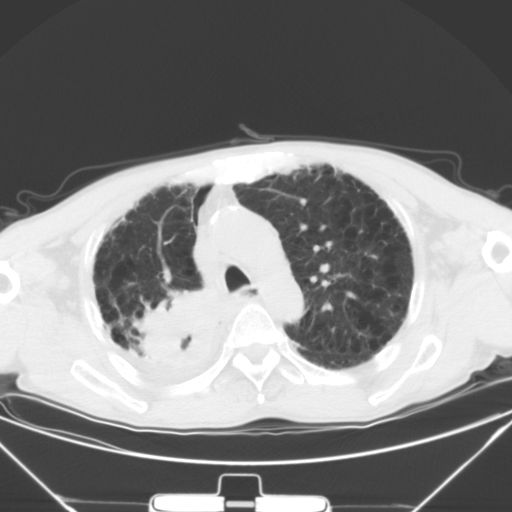
Chest CT, one axial slice. Position 35 of 50 along the scan axis. Lung window (W 1500 / L -600 HU). 5 mm slice thickness. 512 × 512 image matrix. Patient: male, 65 years. Case-level facts recorded for this patient, not image findings: clinical TNM (as recorded): T3 N1 M1a.
Structures marked on this image (rectangle marked by the reading radiologist):
- lung tumour (recorded histology: squamous cell carcinoma): bounding box <137,291,230,380> (left, top, right, bottom; pixels)